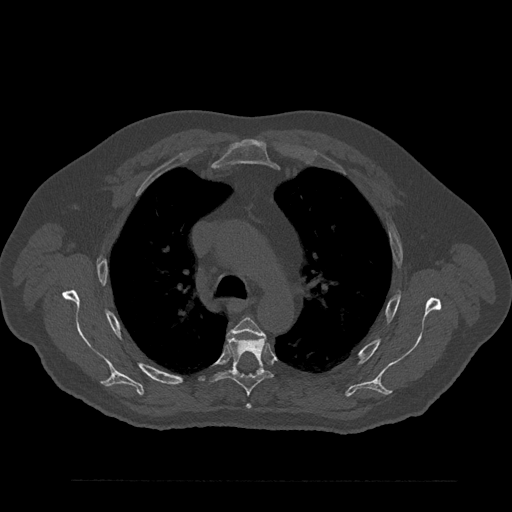
CT including the spine, one axial slice; position 608 of 797 along the scan axis; reconstruction kernel Br40s/3; 120 kVp; bone window (W 1800 / L 400 HU); 0.5 mm slice thickness; 512 × 512 image matrix, field of view 430 × 430 mm. Male patient, age 61 years. From the clinical record (not read from this slice): primary cancer: prostate.
Outlined on this slice (semi-automatically segmented with operator editing):
- T4 vertebra: bounding box <232,318,266,409> (left, top, right, bottom; pixels)
- T5 vertebra: <209,336,273,396>